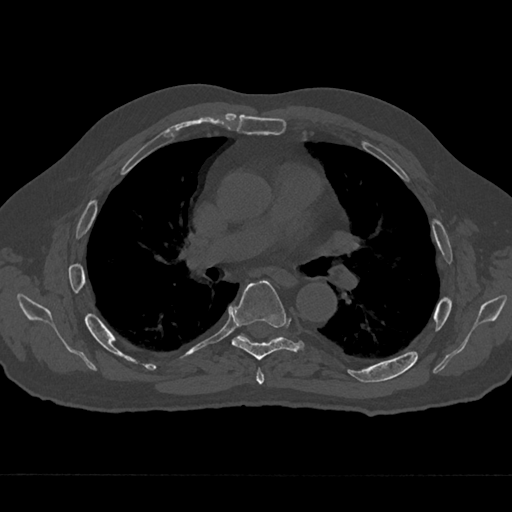
CT including the spine, one axial slice; position 419 of 797 along the scan axis; reconstruction kernel Br40s/3; 120 kVp; bone window (W 1800 / L 400 HU); 0.5 mm slice thickness; 512 × 512 image matrix. Male patient, age 75 years. From the clinical record (not read from this slice): primary cancer: renal; vertebrae with lytic lesions (as recorded): T4.
Structures marked on this image (semi-automatically segmented with operator editing):
- T5 vertebra: bounding box [x1, y1, x2, y2] px = [256, 368, 264, 385]
- T6 vertebra: [232, 280, 305, 360]